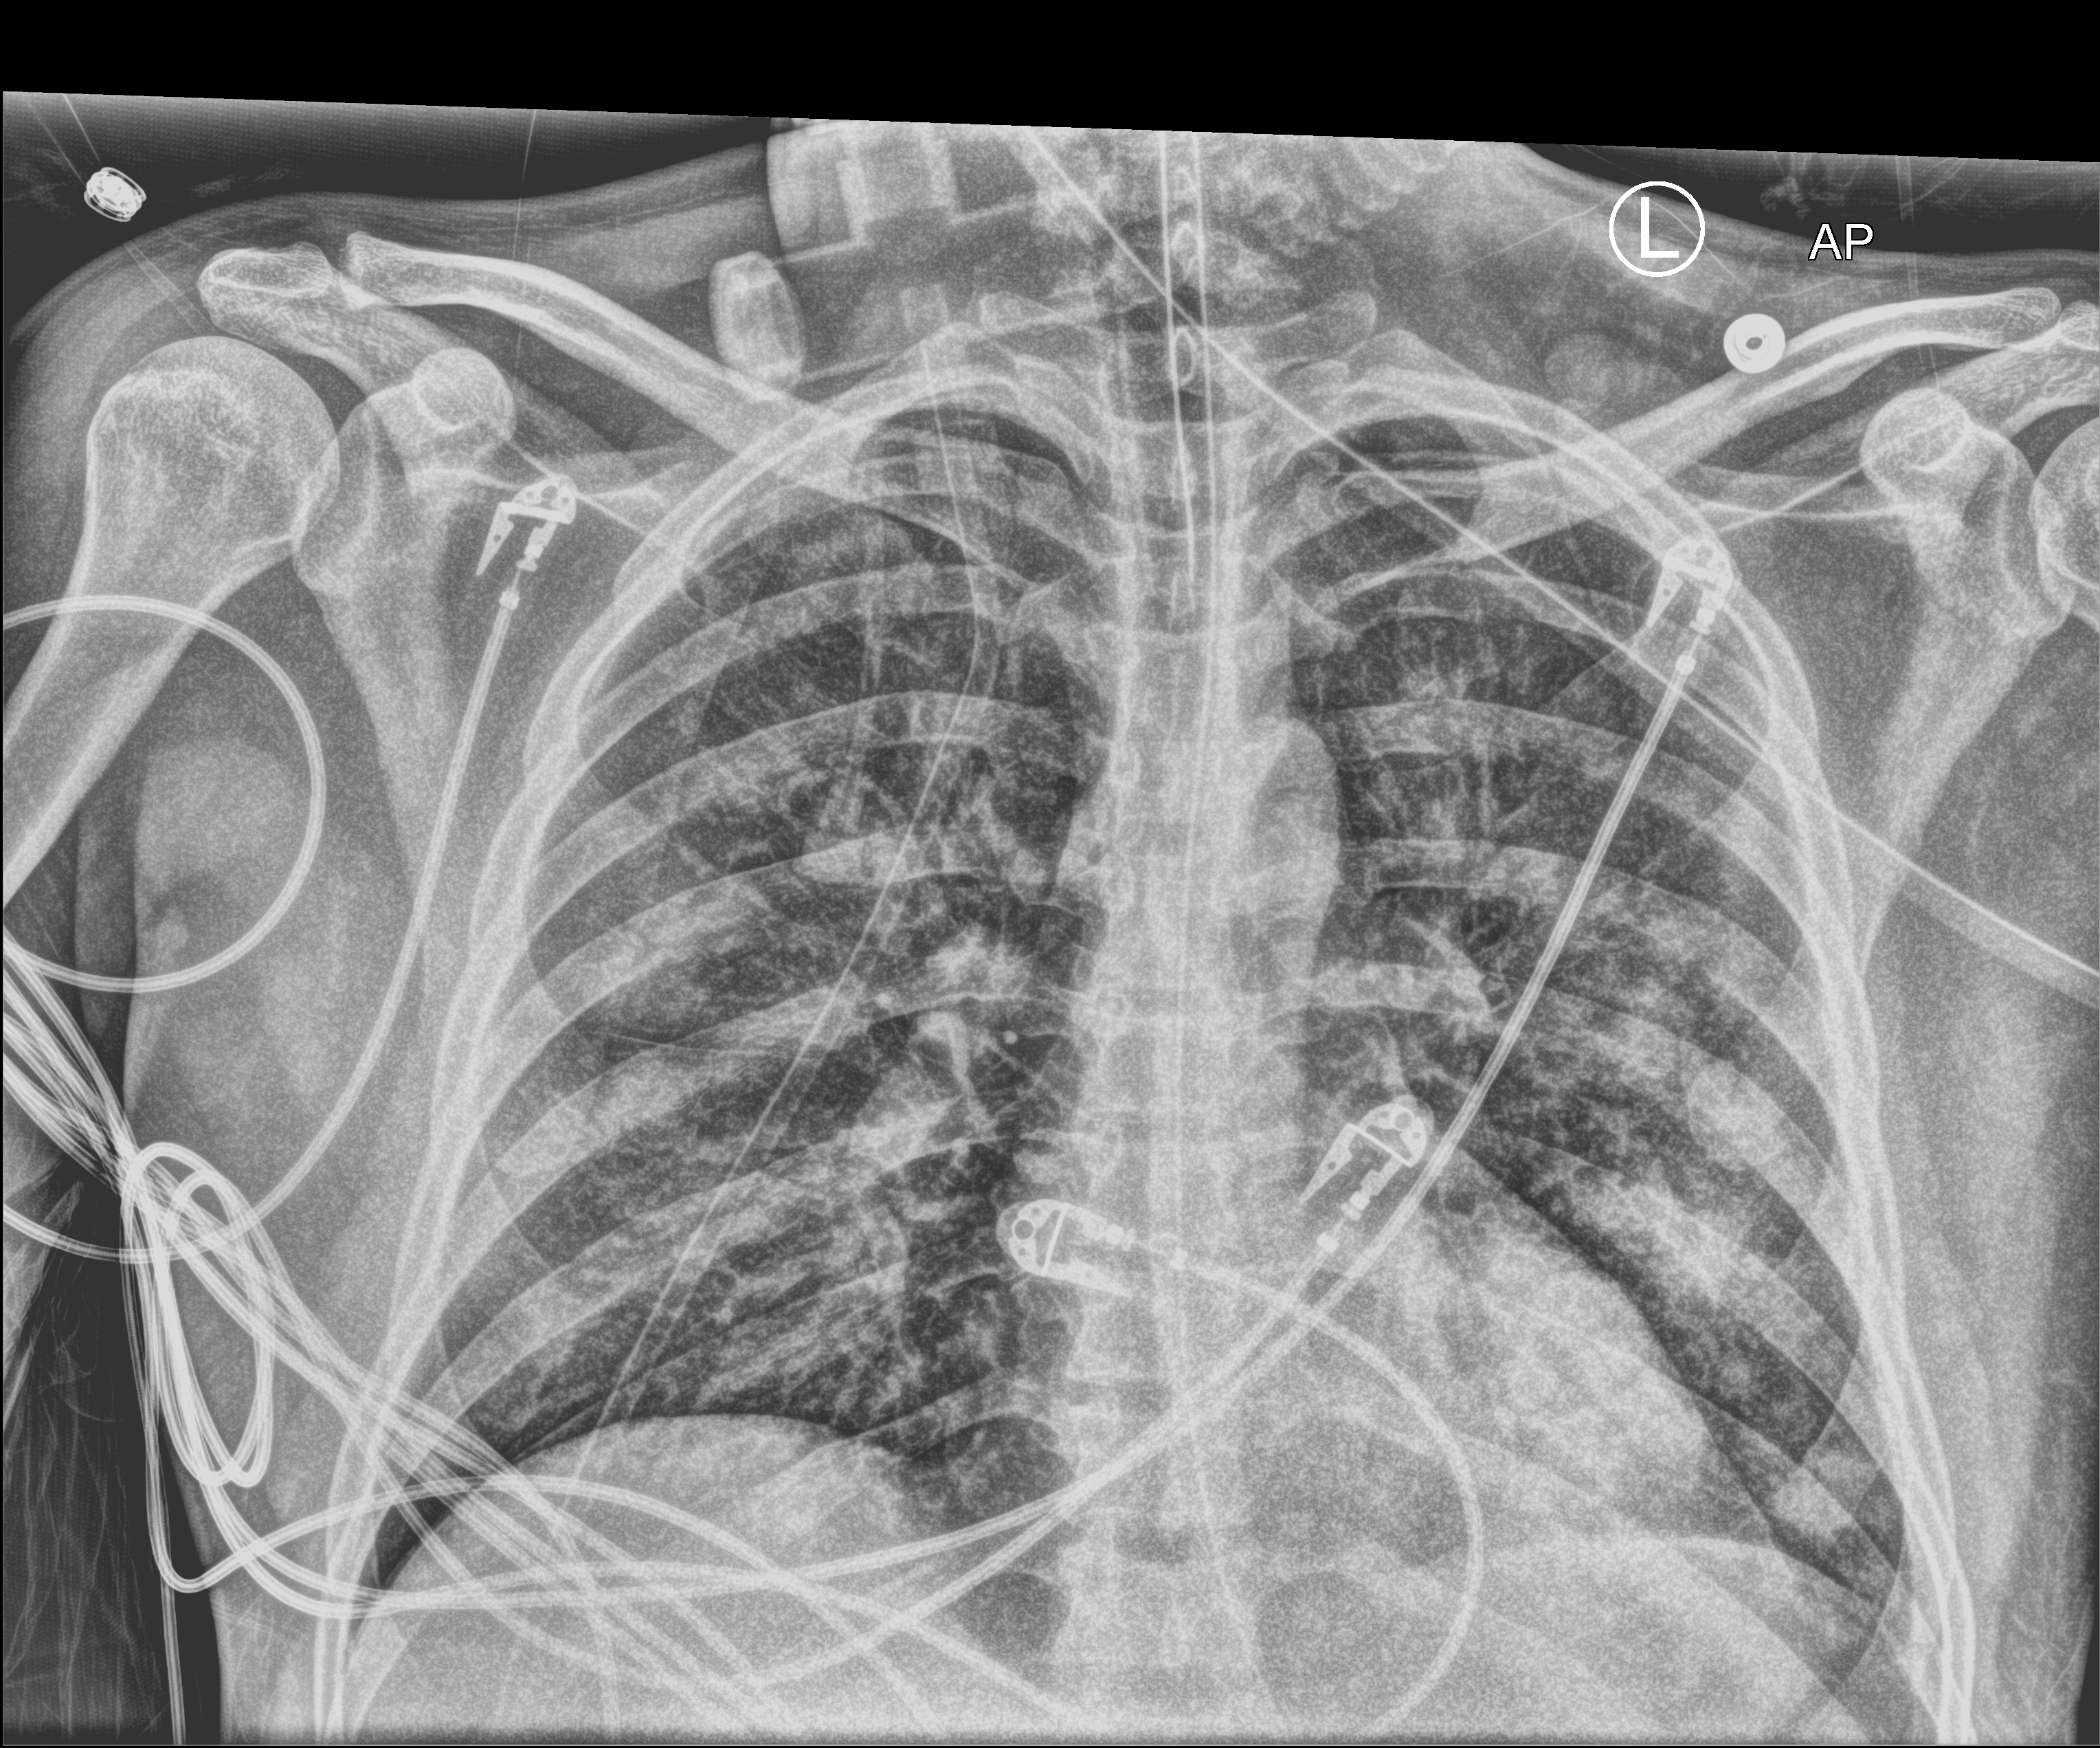
Portable chest radiograph, anteroposterior (AP) projection. Patient hospitalised with COVID-19; male, aged 18–59 years.
From the hospital-stay record, not from the radiograph (when in the stay this image was taken is not recorded):
- other chronic lung disease (admission record): no